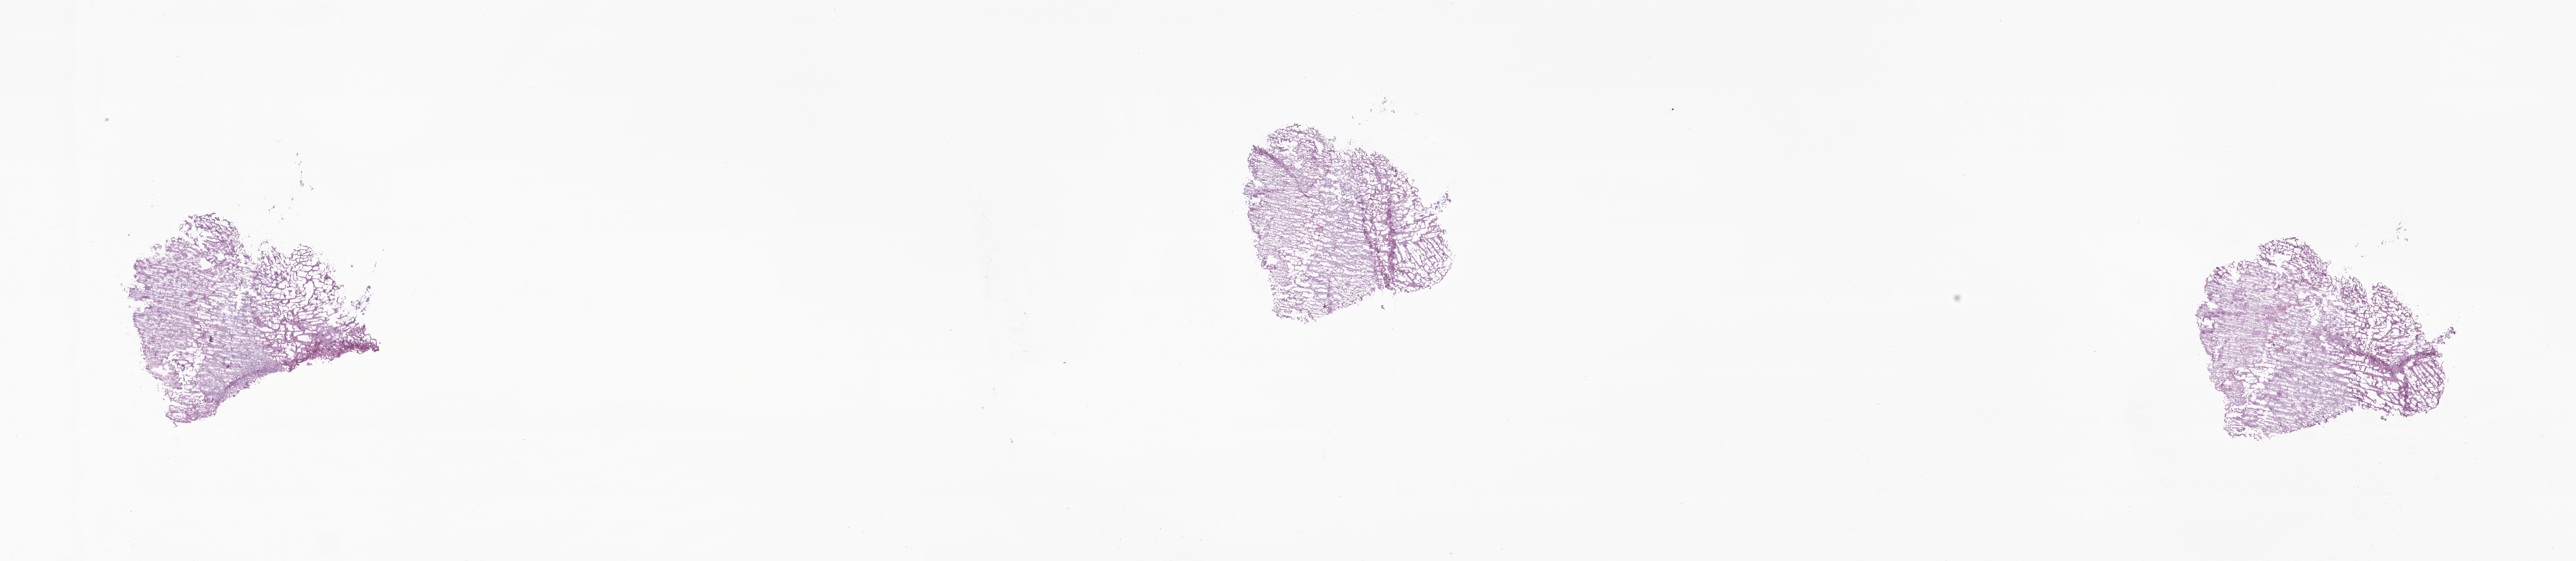
Whole-slide image, haematoxylin and eosin stain of tumor tissue from the temporal lobe, shown as a low-resolution overview of the whole scanned area (about 41.2 x 9.0 mm). Cryosection (OCT / tissue freezing medium). Female patient, age 848 days (about 2.3 years).
Diagnosis (ICD-O-3 morphology term): Ganglioglioma, NOS.